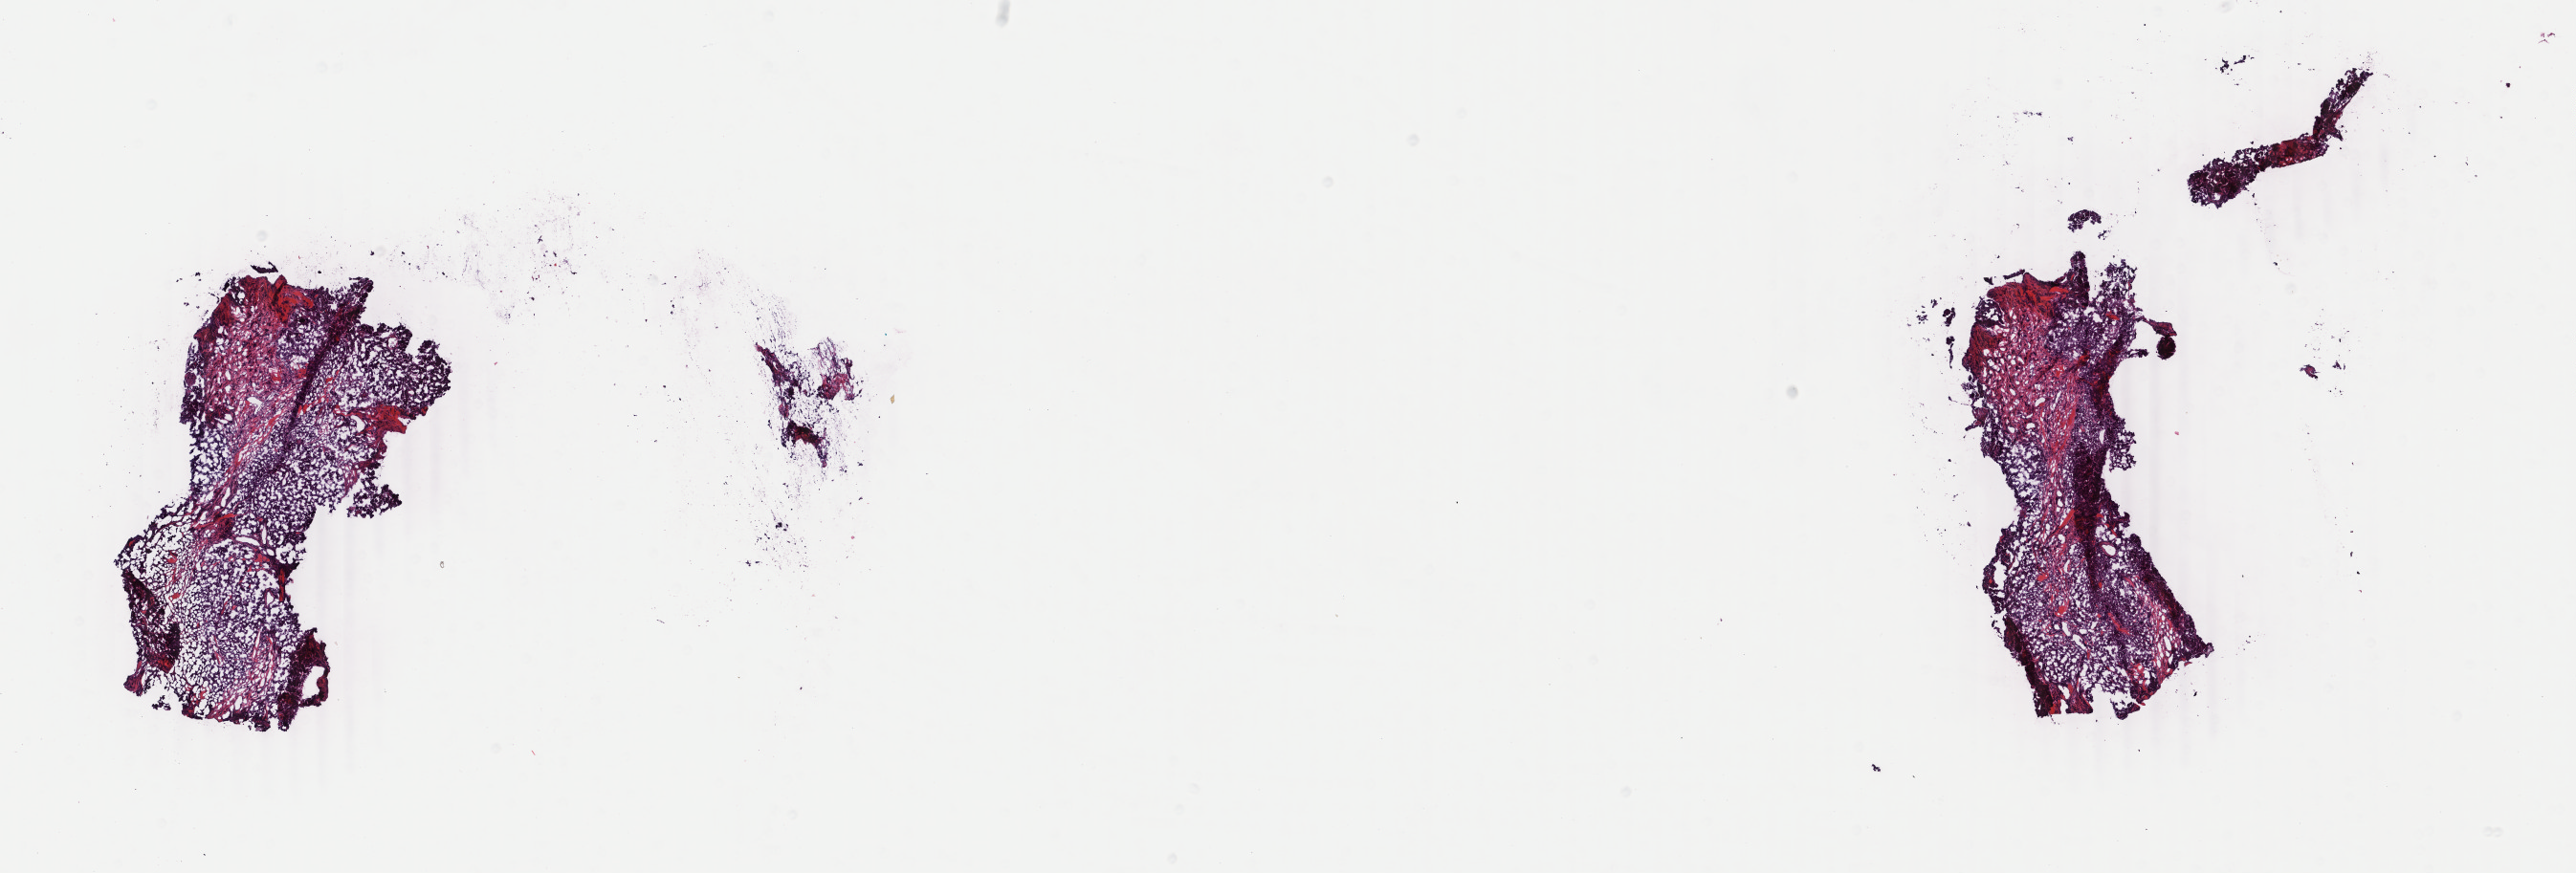
Whole-slide histology image, H&E-stained — a low-resolution overview of the entire scanned area, about 21.4 x 7.3 mm (acquisition: 40x scan), frozen section from the bottom of the tissue portion, breast, primary tumour sample. Patient: female, age at initial diagnosis 45 years. Composition of this section per pathologist review: tumour cells 85%, tumour nuclei 85%, normal cells 0%, stromal cells 15%, necrosis 0%. Infiltration values recorded for this section: lymphocyte infiltration 1%, monocyte infiltration 0%, neutrophil infiltration 0%.
Diagnosis: Infiltrating duct carcinoma, NOS. AJCC pathologic stage: IA. Laterality: left.